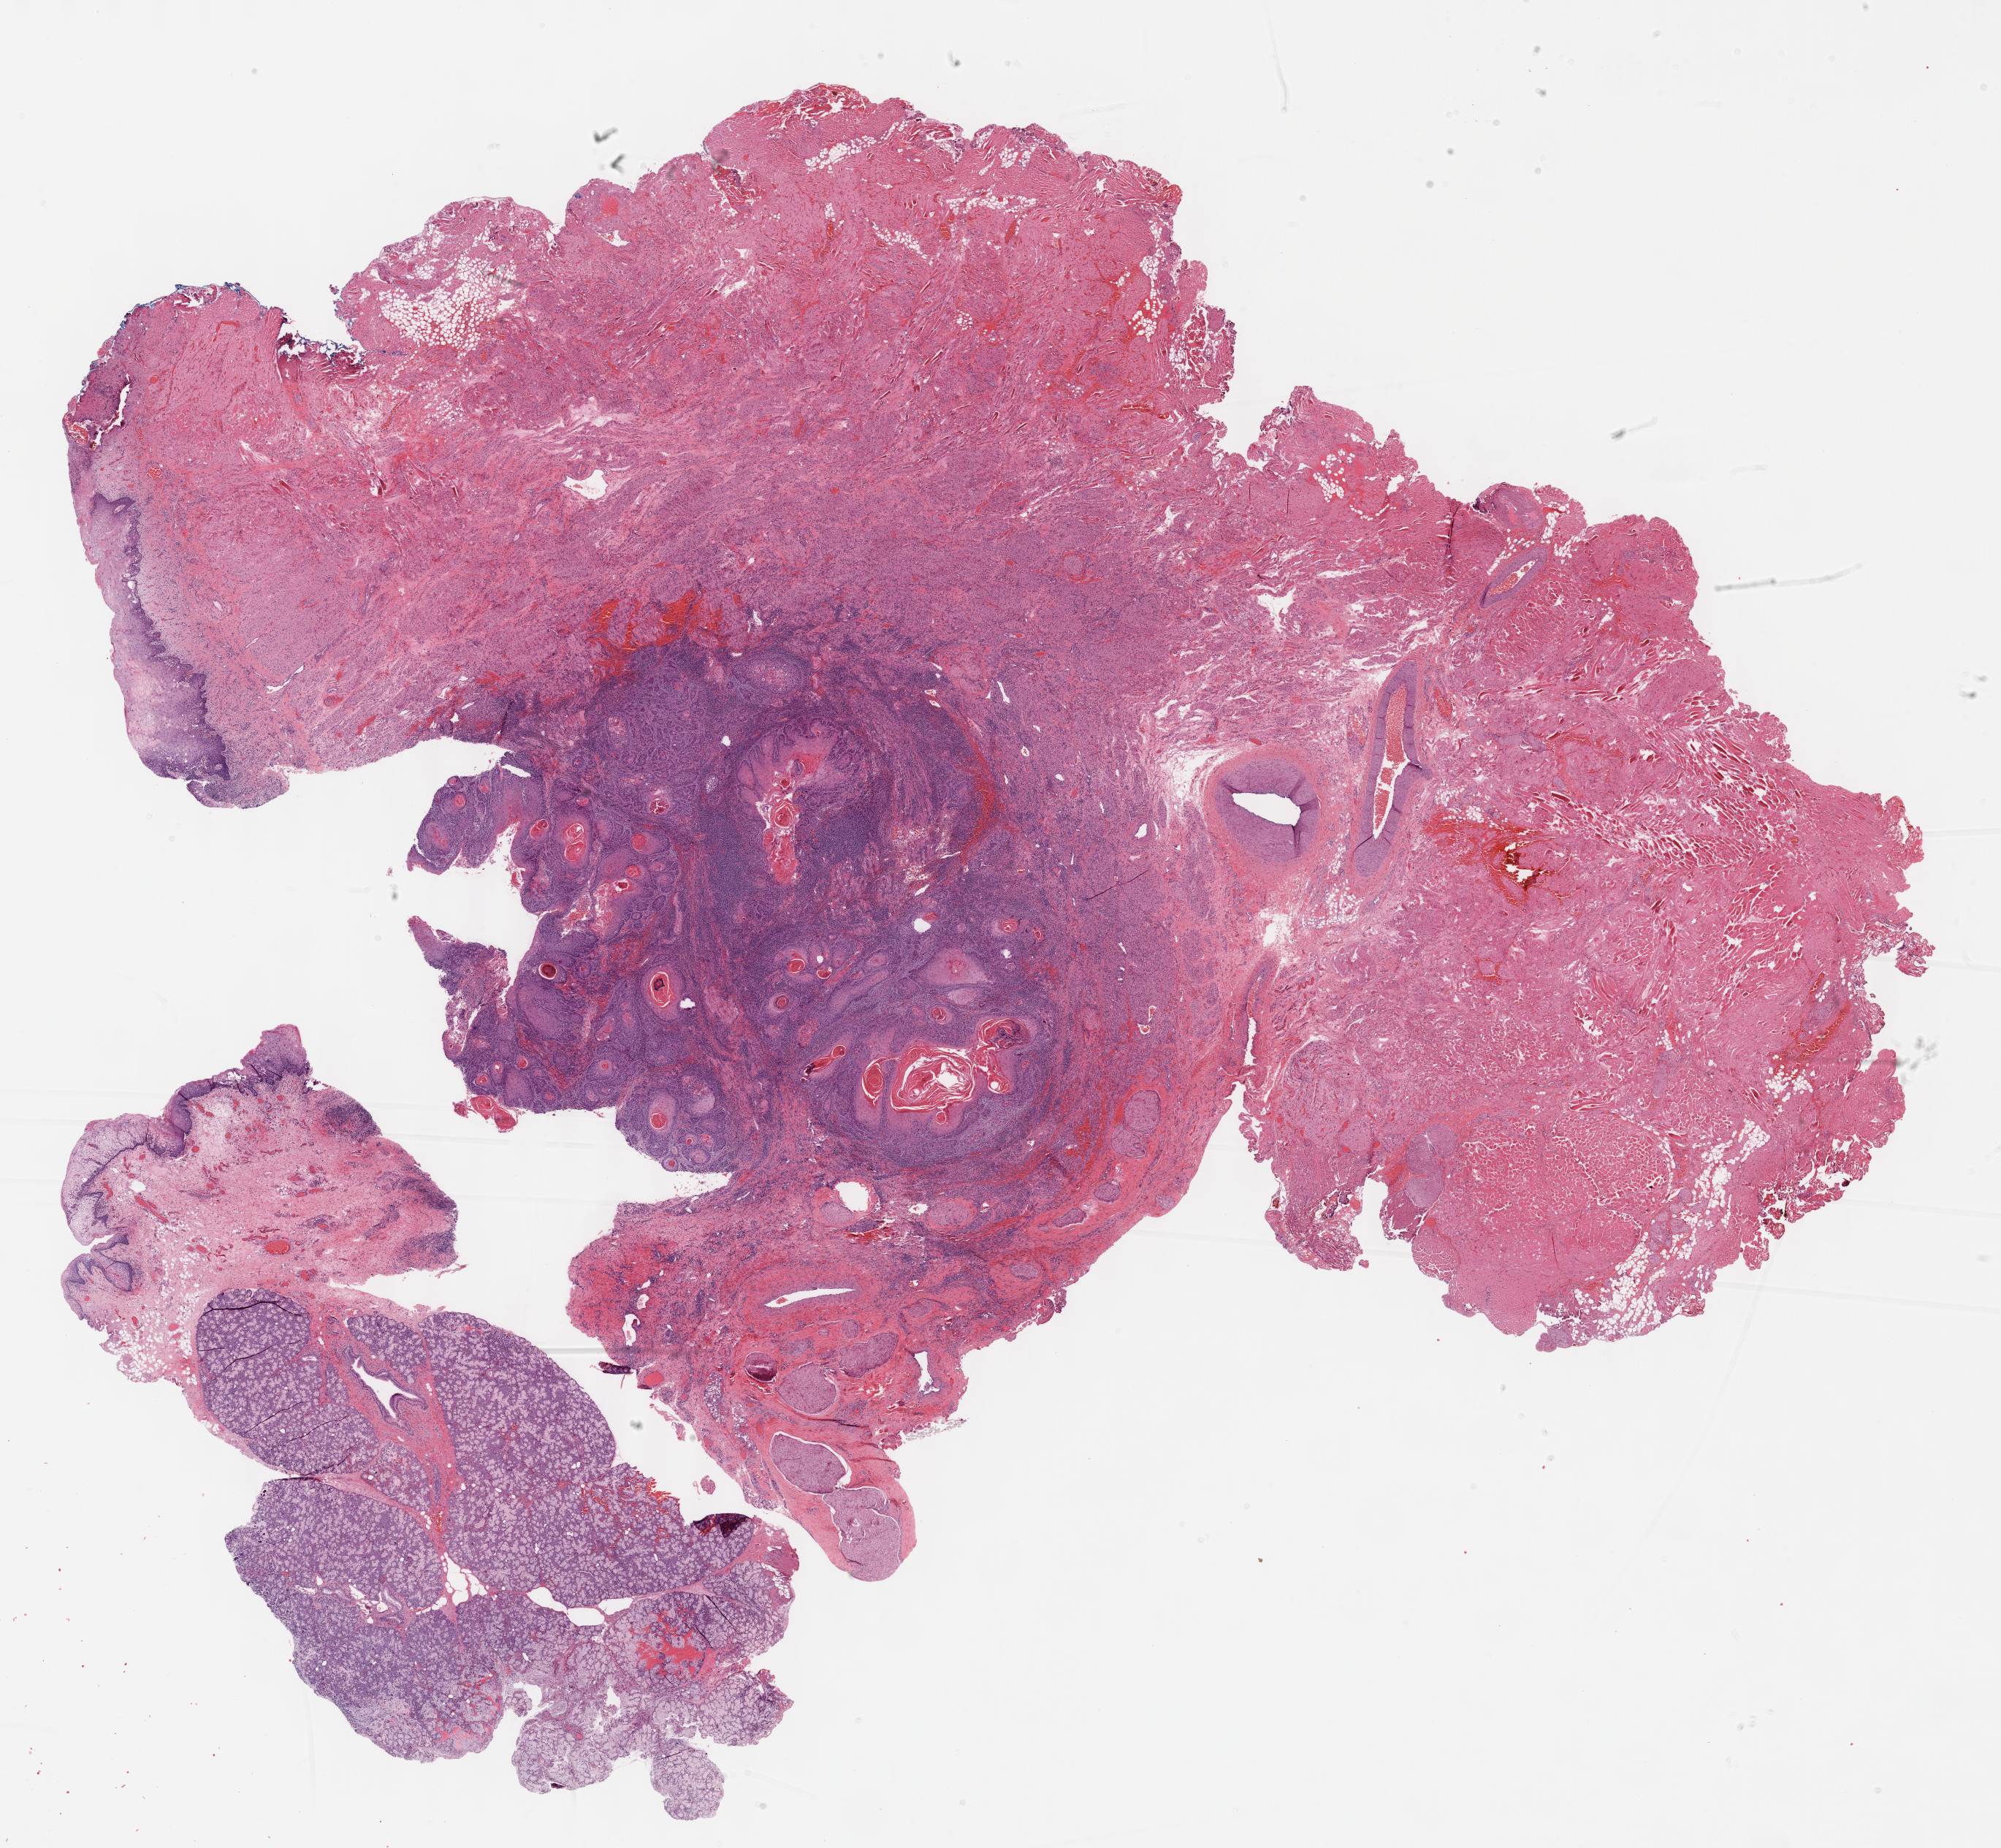
Whole-slide histology image, Hematoxylin and eosin (H&E) stained, a low-resolution overview of the entire scanned area, about 22.1 x 20.4 mm (from a 40x scan); formalin-fixed paraffin-embedded (FFPE) diagnostic section; primary tumour sample from the head and neck. Male patient; age at initial diagnosis 24 years. Histologic grade: G1 (well differentiated).
AJCC pathologic stage: III (6th edition). Laterality: right. Pathologic diagnosis: Squamous cell carcinoma, NOS (tongue, NOS).